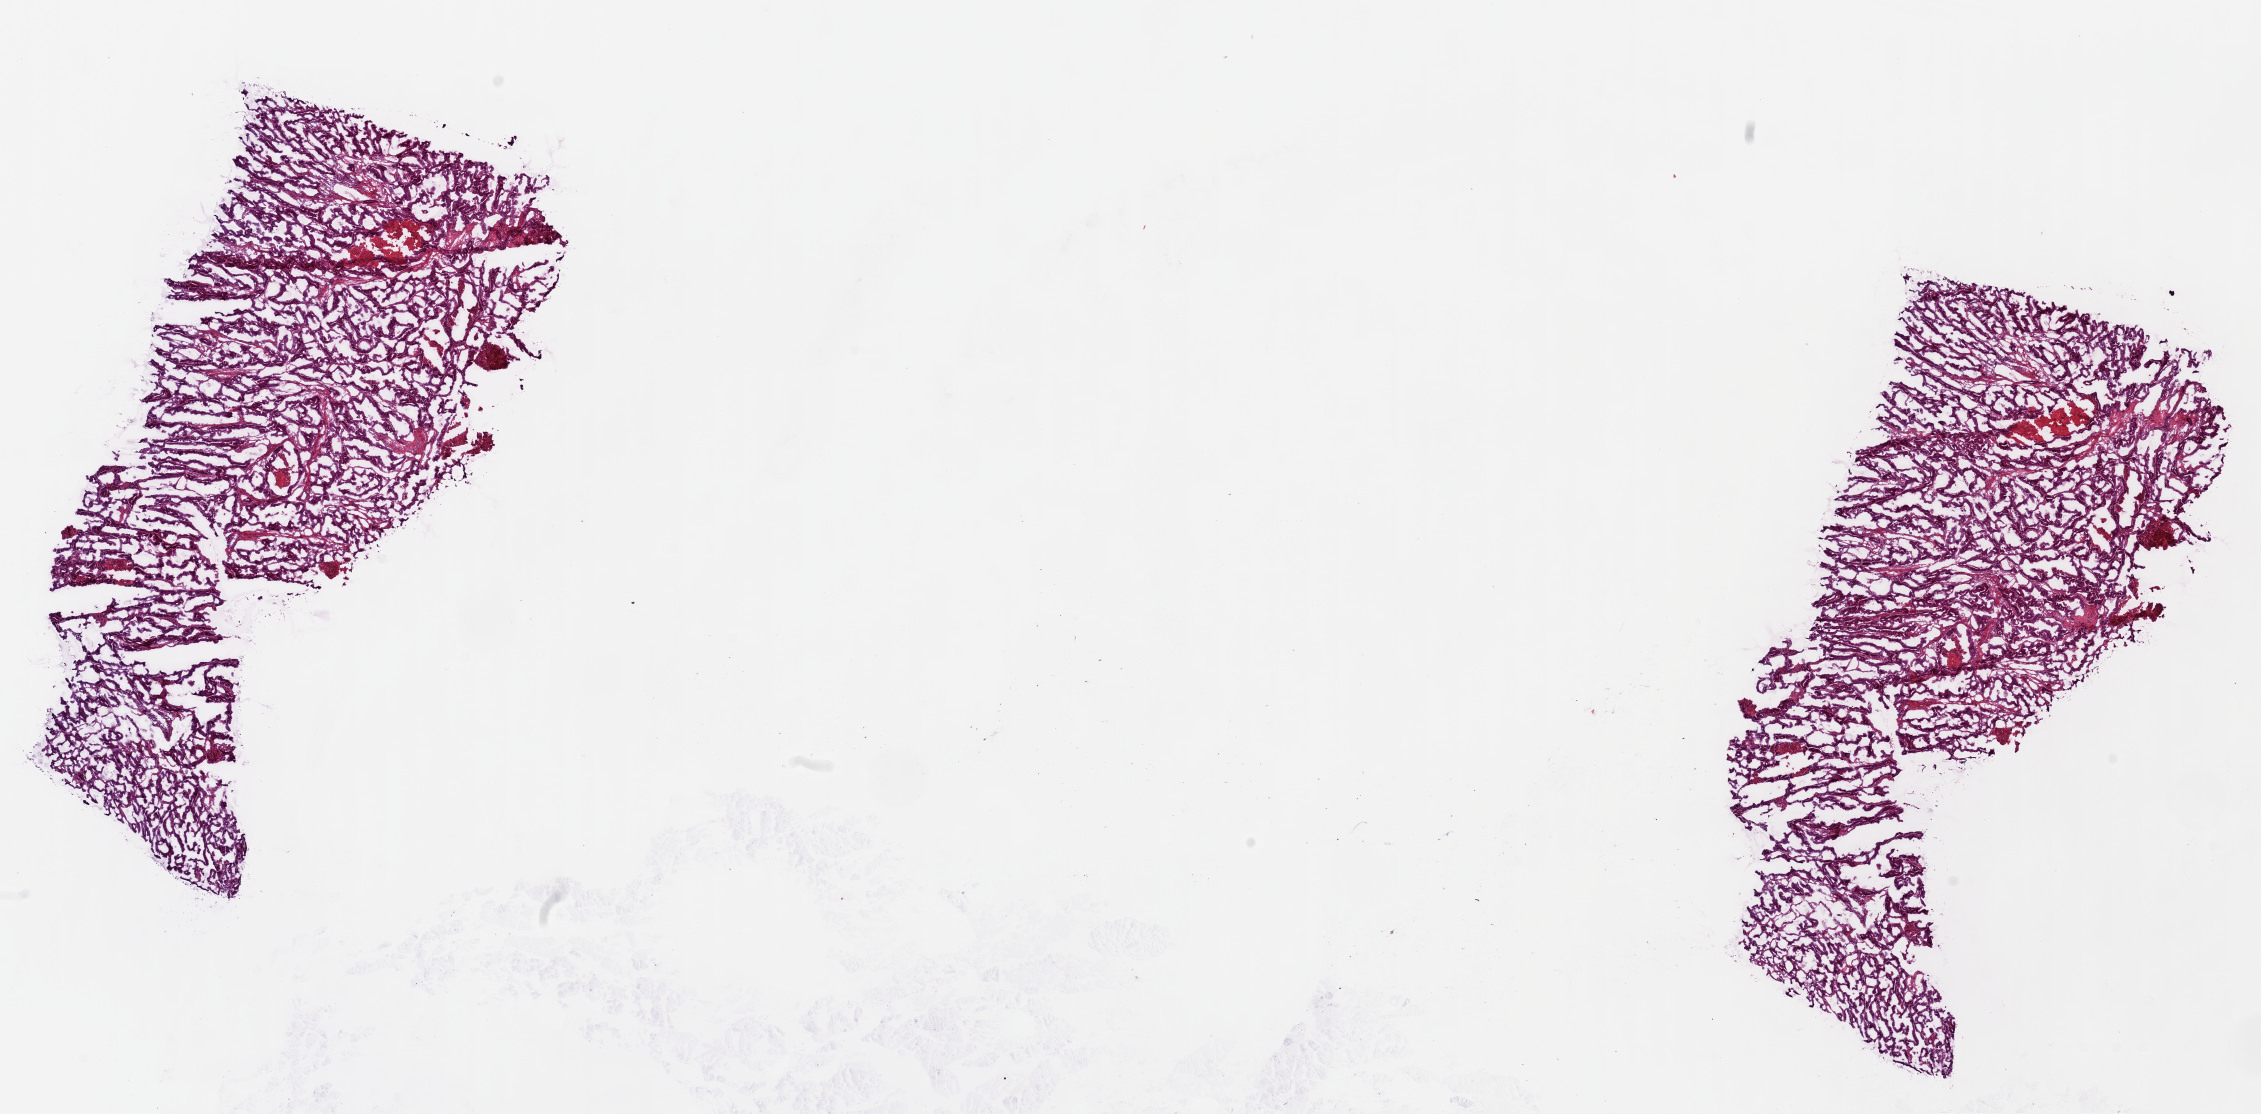
Whole-slide histology image, H&E — low-resolution overview of the scanned area, about 17.9 x 8.8 mm (from a 40x scan); frozen section from the top of the tissue portion; sample: primary tumour, colon. Patient: female, age at initial diagnosis 72 years. Slide review estimates, as recorded: tumour cells 80%, tumour nuclei 80%, normal cells 0%, stromal cells 17%, necrosis 3%. Infiltration values recorded for this section: lymphocyte infiltration 2%, monocyte infiltration 1%, neutrophil infiltration 1%.
Pathologic diagnosis: Adenocarcinoma, NOS (sigmoid colon). Lymph nodes positive (case pathology): 0 of 15 examined. AJCC pathologic stage: IIA.